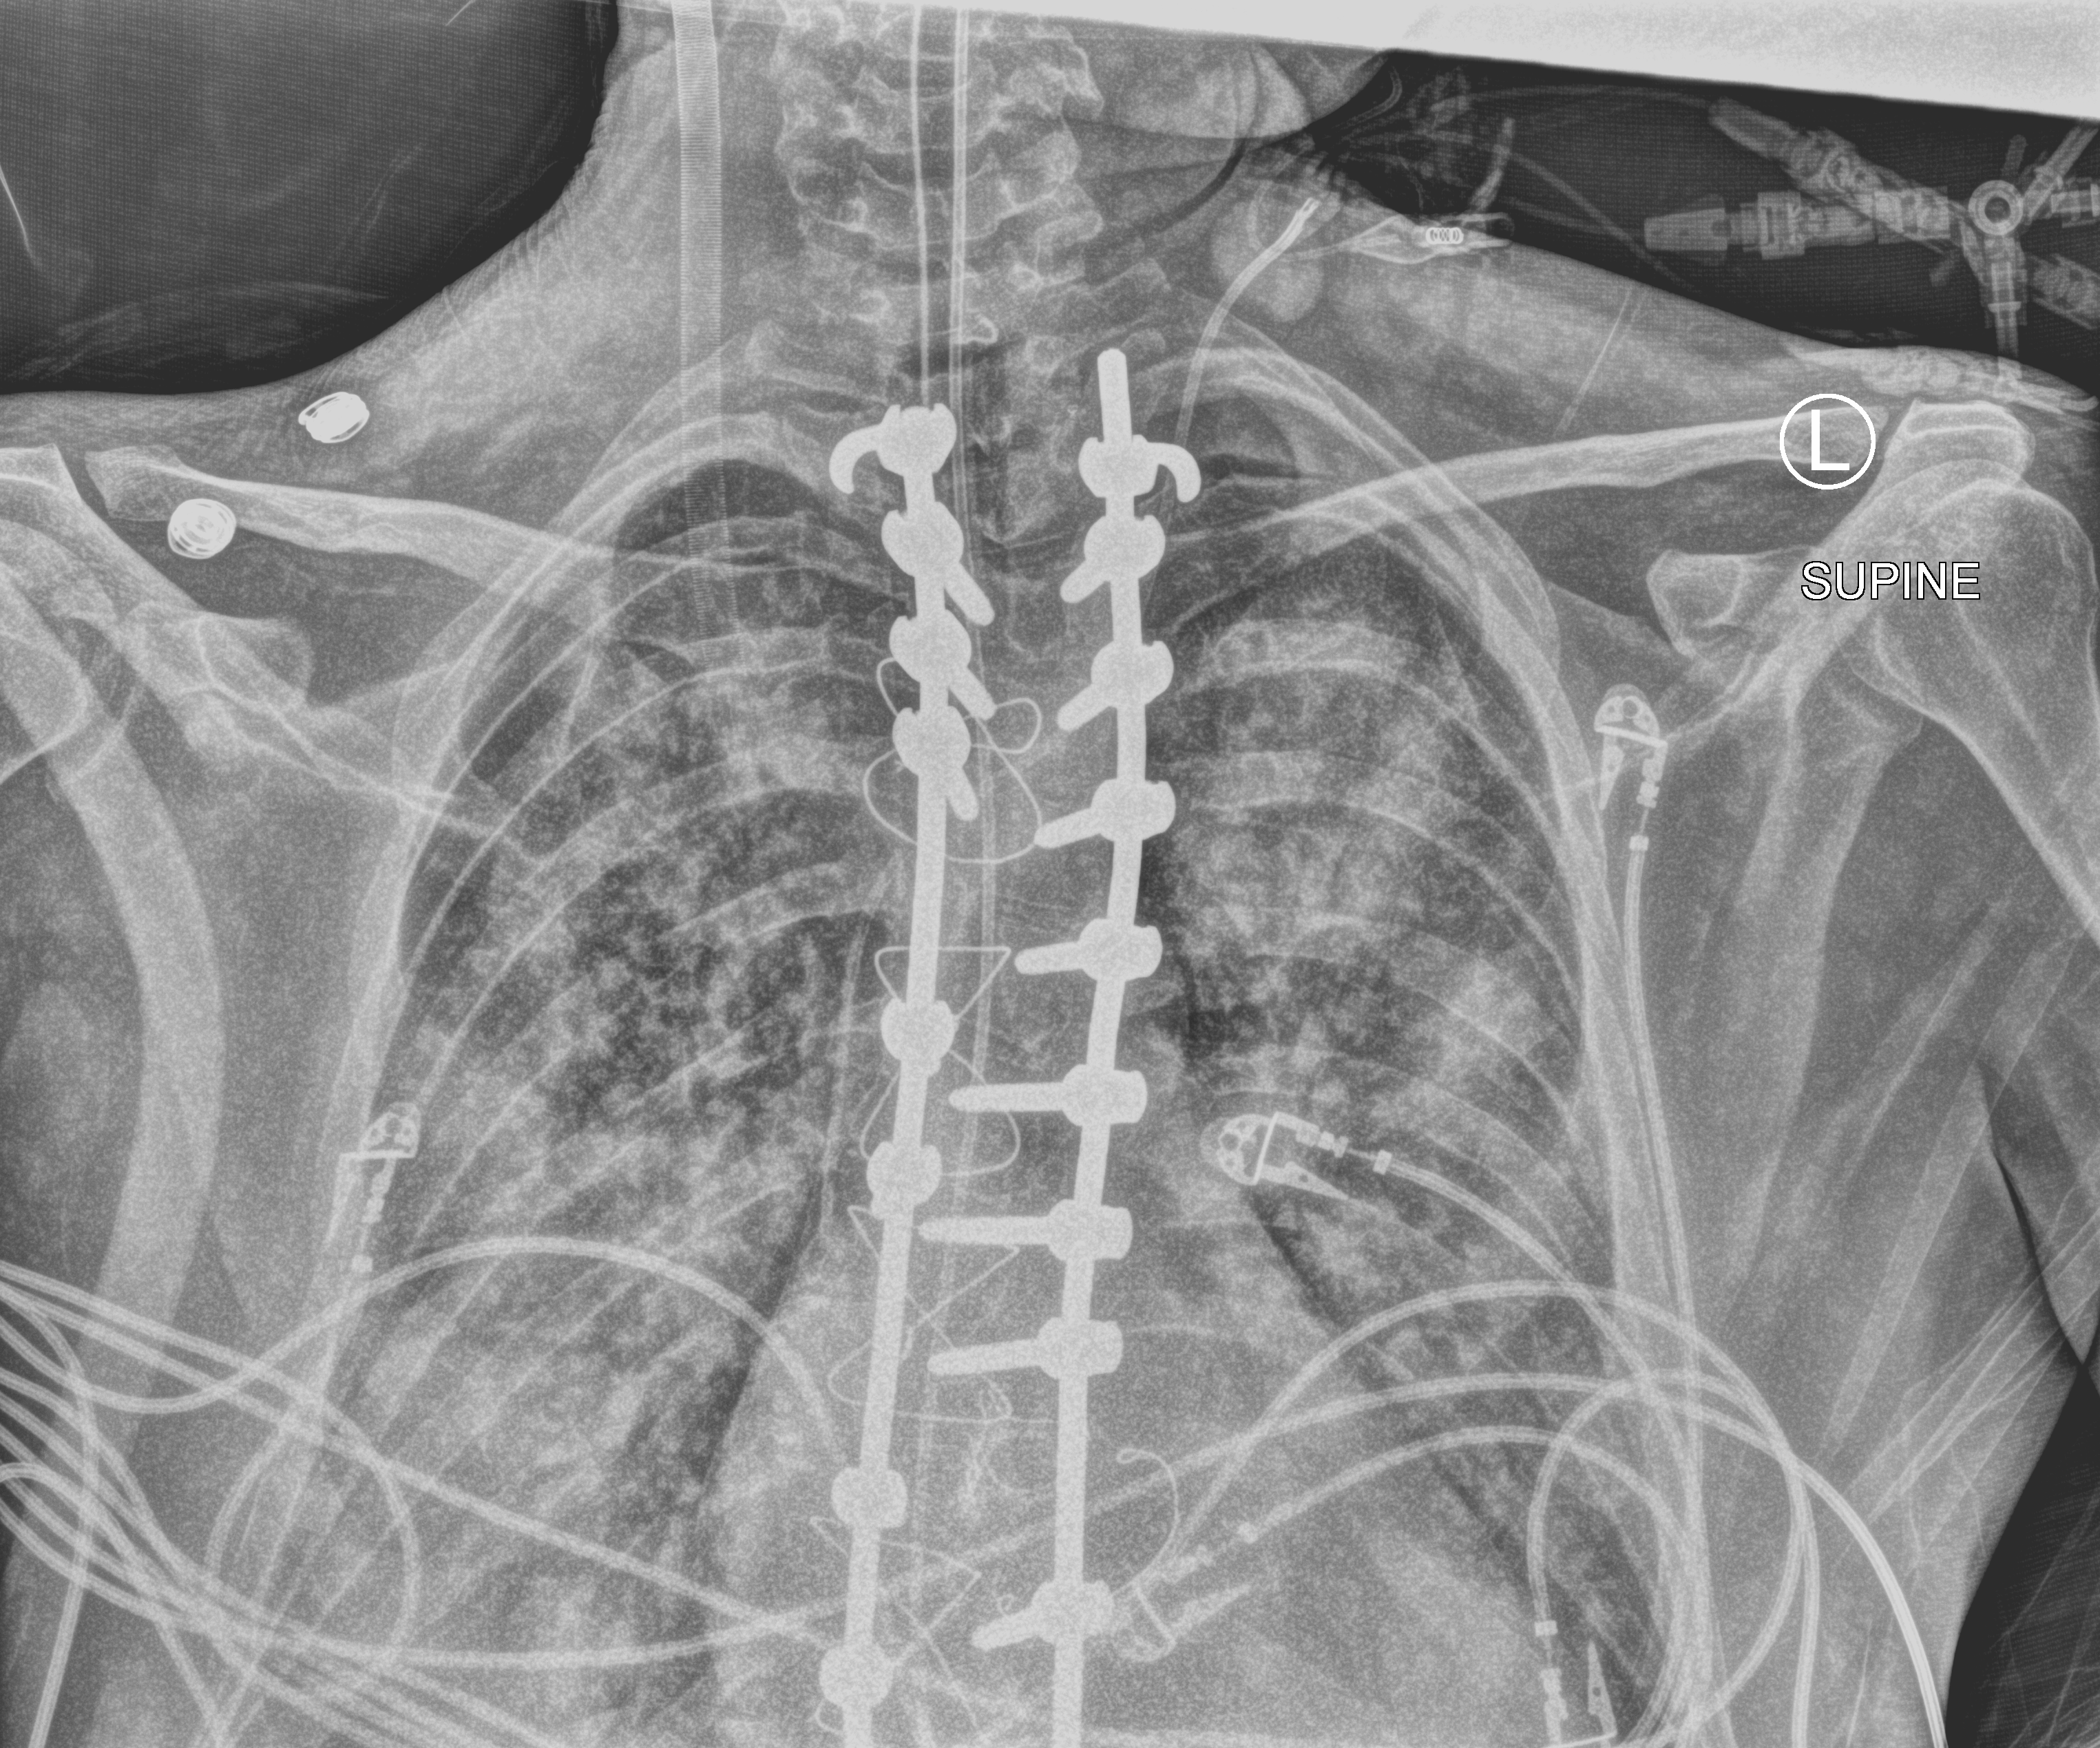
Bedside chest radiograph (computed radiography). Patient hospitalised with COVID-19, aged 18–59 years.
Hospital-stay facts (about this admission, not read from this image; timing relative to this image not recorded):
- chronic kidney disease (admission record): no
- admitted to intensive care during this hospital stay: yes
- mechanically ventilated during this hospital stay: yes